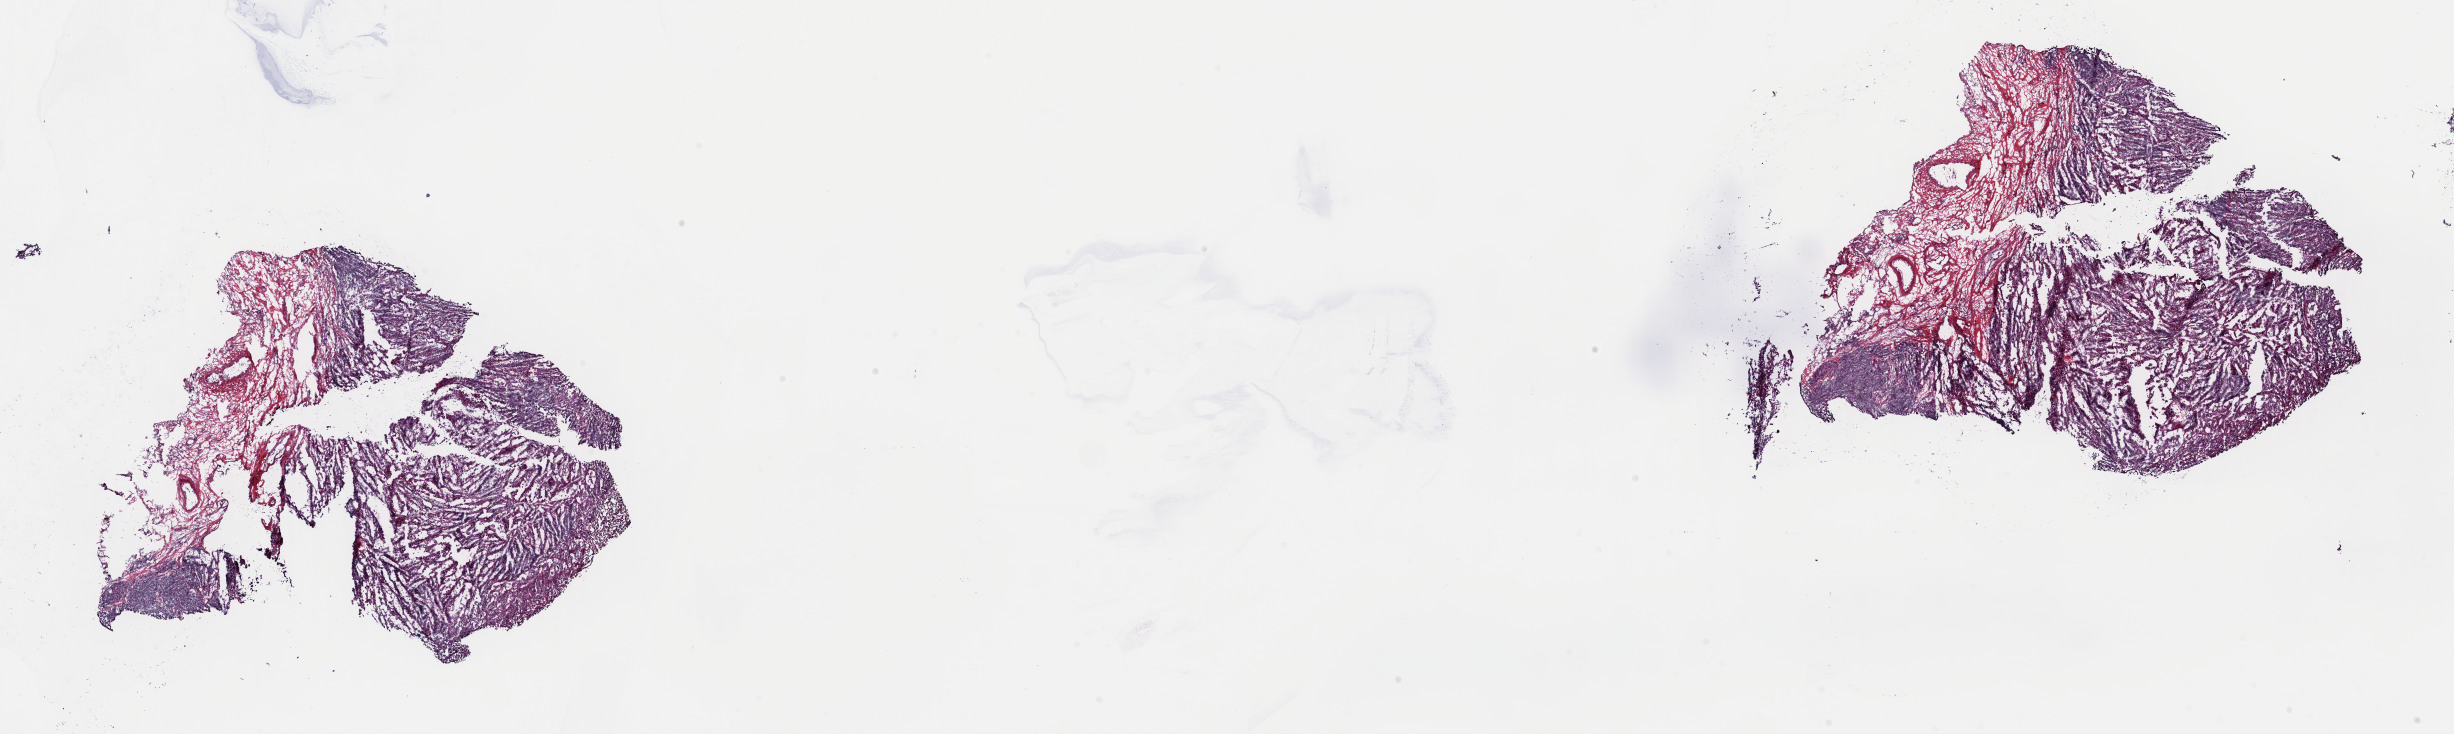
Whole-slide histology image, Hematoxylin and eosin (H&E) stained — low-resolution overview of the scanned area, about 38.8 x 11.6 mm. Frozen section. Metastatic tumour sample, sampled site not recorded. Patient: male, age at initial diagnosis 60 years. Composition of this section per pathologist review: tumour cells 100%, tumour nuclei 75%, normal cells 0%, stromal cells 0%, necrosis 0%. Infiltration values recorded for this section: lymphocyte infiltration 10%, monocyte infiltration 2%, neutrophil infiltration 0%.
- this section: metastatic tumour tissue
- patient diagnosis: Malignant melanoma, NOS